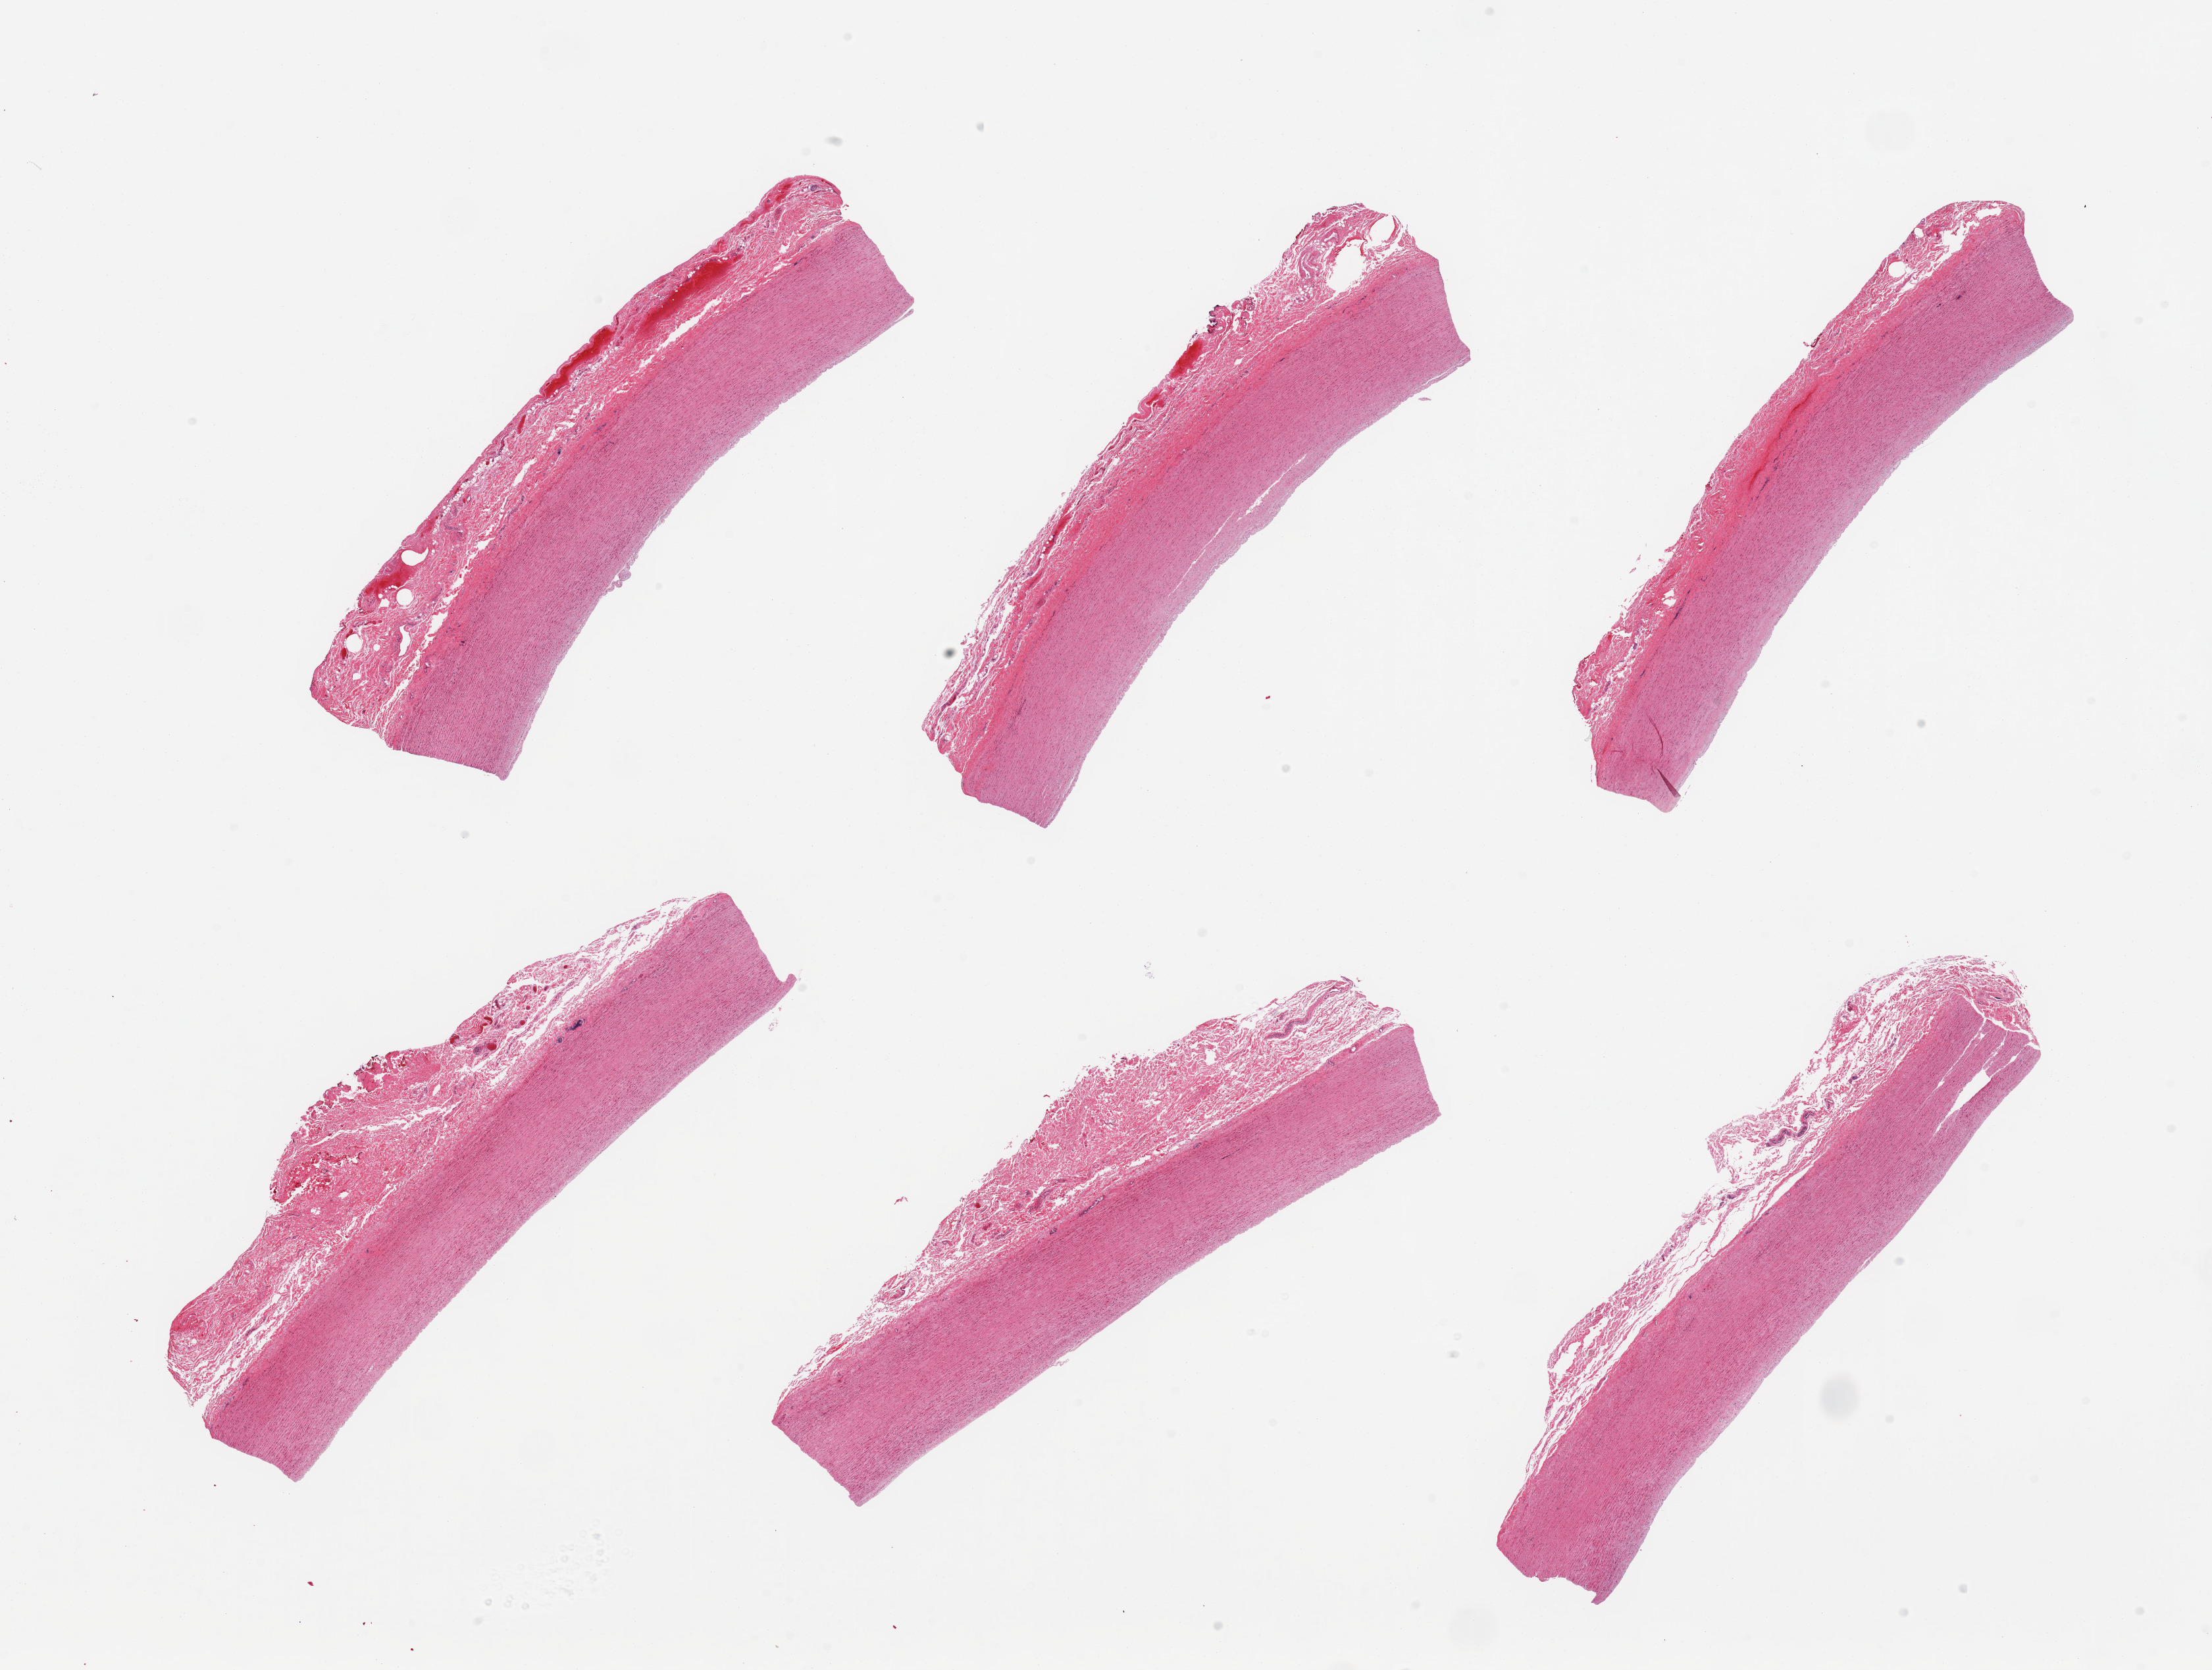
Digitized hematoxylin and eosin (H&E)-stained section, brightfield — shown as a low-resolution overview of the whole scanned area (about 26.6 x 20.1 mm), PAXgene-fixed, paraffin-embedded tissue, sampled site (target tissue): aorta, tissue donor sample. Donor sex: male.
Pathologist's review note for this sample: 6 pieces; 1.5mm of attached adventitia.